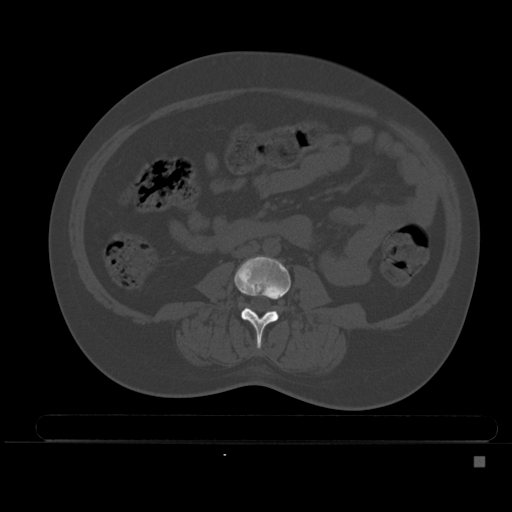
CT including the spine, one axial slice; slice 146 of 495 in the series (ordered by position); bone window (W 1800 / L 400 HU); 1.5 mm slice thickness; 512 × 512 image matrix. Patient: female, 33 years. Case-level facts recorded for this patient, not image findings: primary cancer: breast.
Structures marked on this image (semi-automatically segmented with operator editing):
- L3 vertebra: box from (x=234, y=256) to (x=291, y=348) px